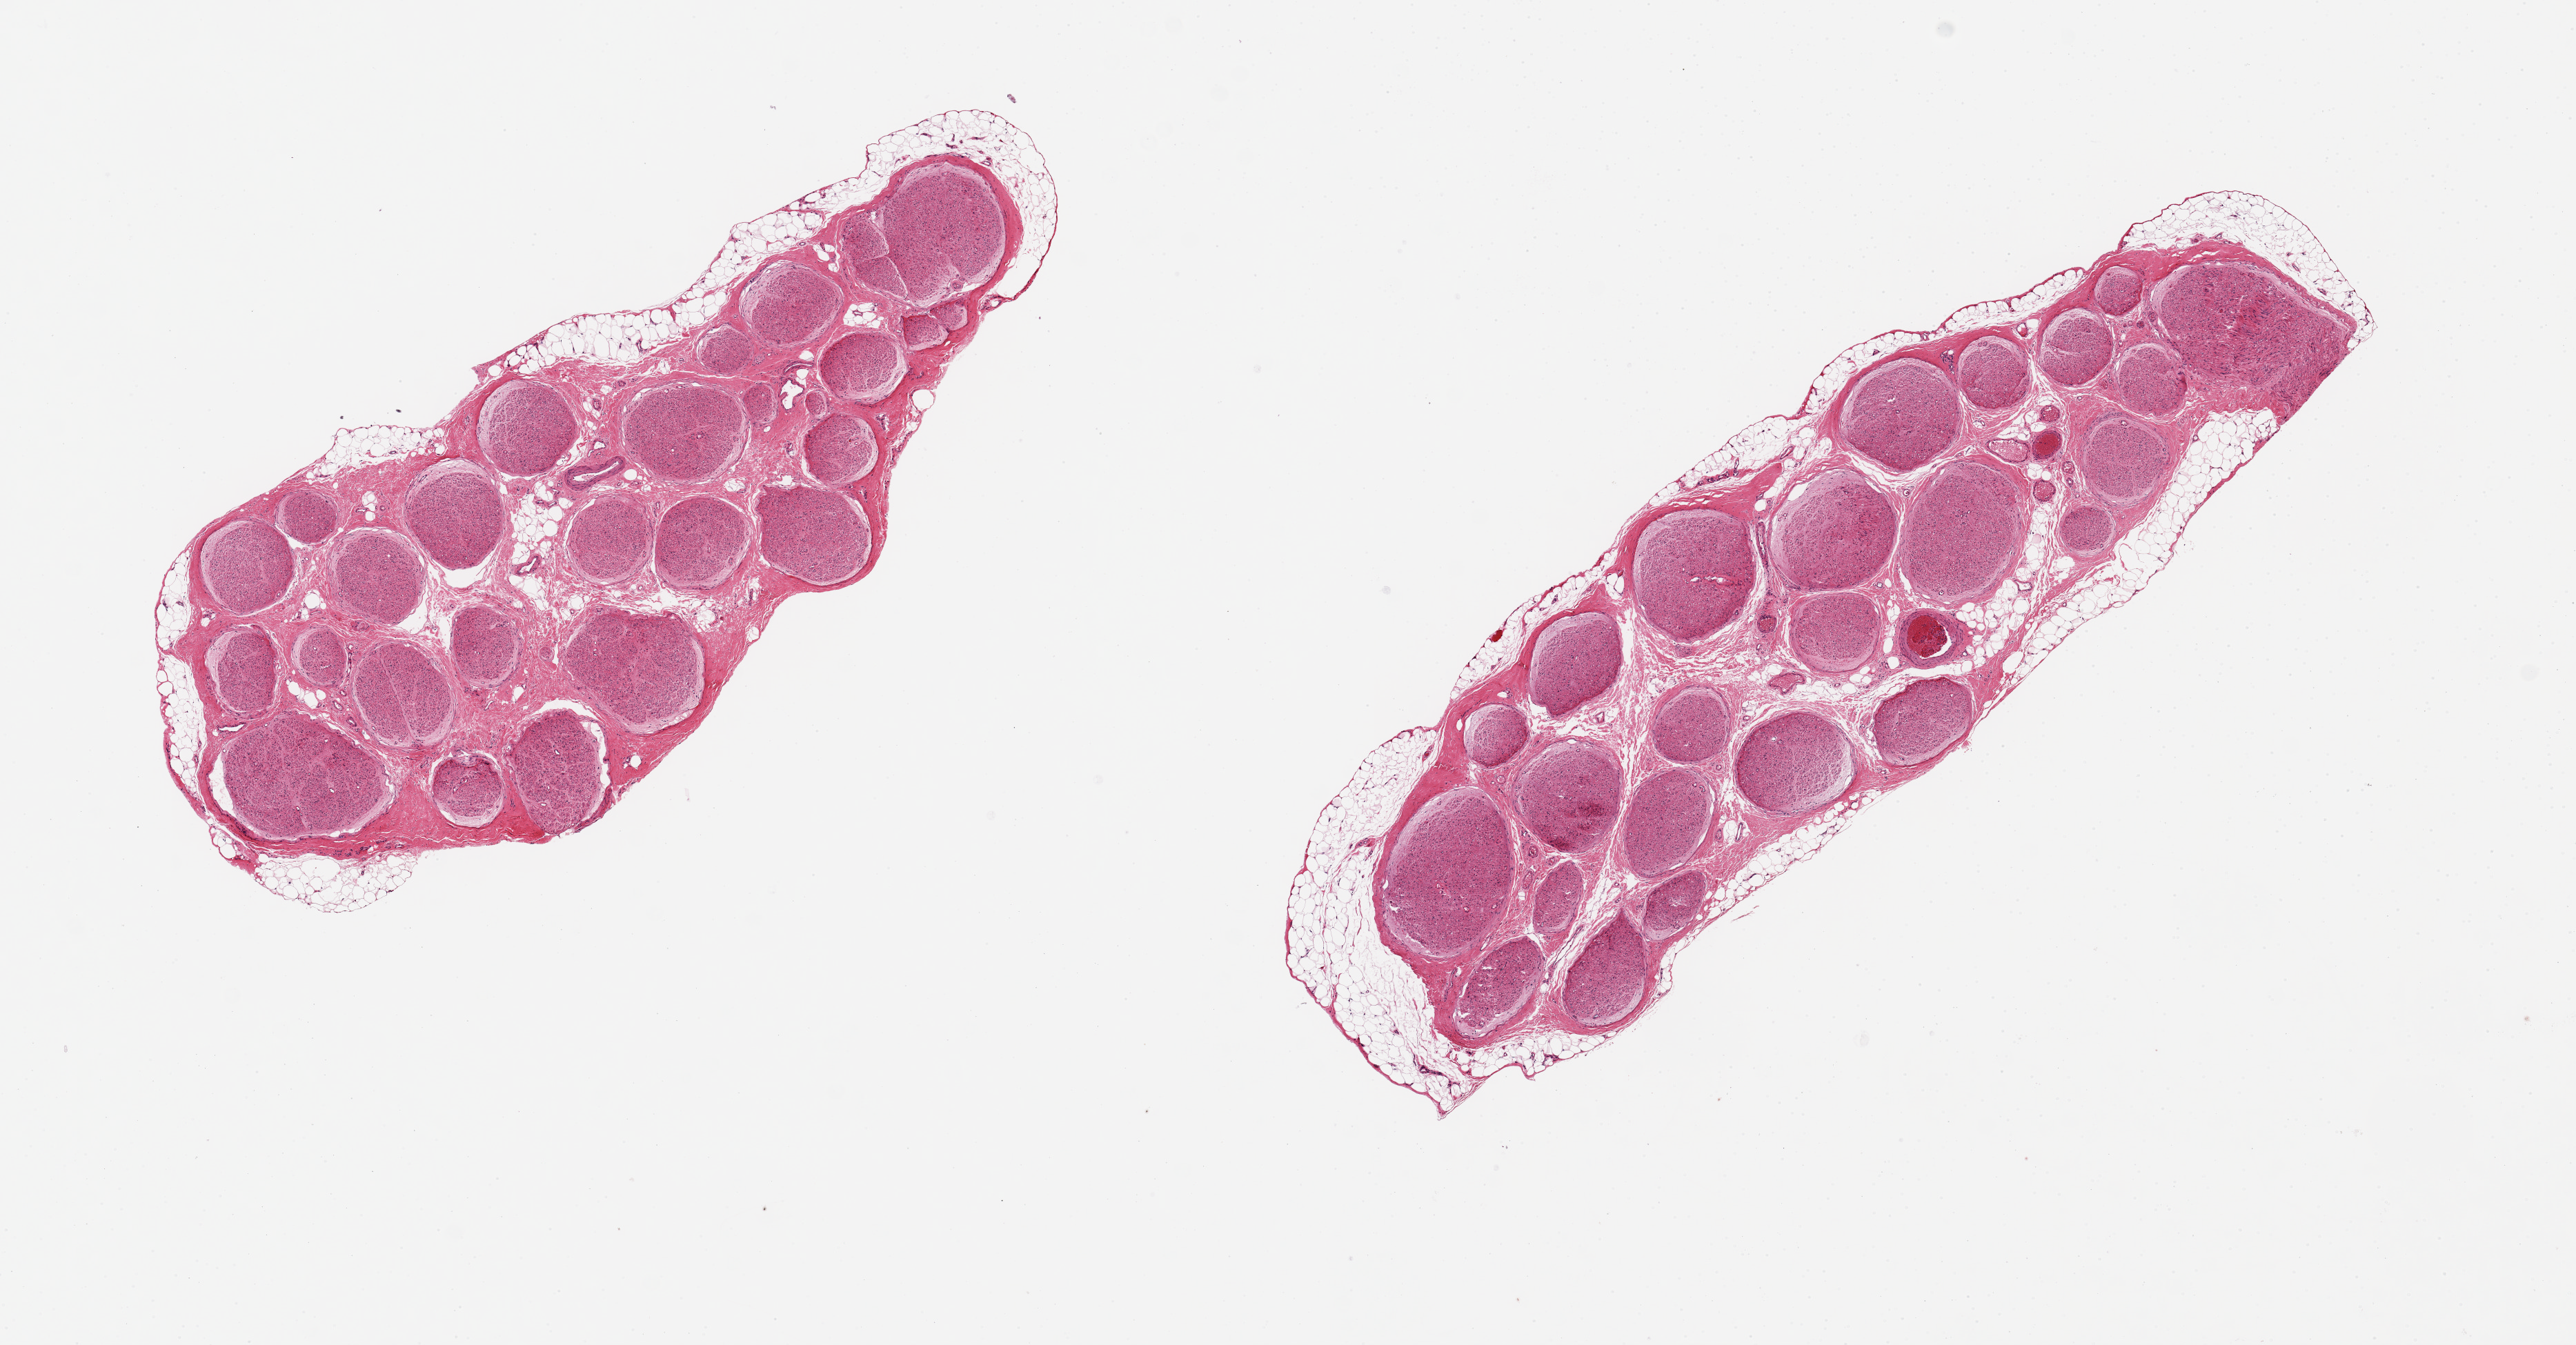
H&E whole-slide image — whole scanned area (about 14.8 x 7.7 mm, acquisition: 20x scan) shown as a low-resolution overview. PAXgene-fixed, paraffin-embedded tissue. Section of tibial nerve (target tissue). Tissue donor sample.
* reviewer comment on this tissue sample: 2 aliquots, ~6x2.5mm. Minimal dicontinuous adhernet fat, up to 0.5mm